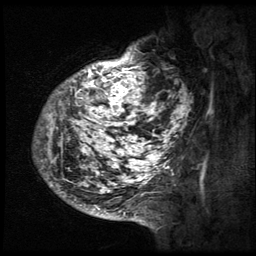
Breast MRI (dynamic contrast-enhanced), one sagittal slice. 3 images stored at this slice position (order not interpretable as contrast timing). 1.5 T. TE 4.2 ms, TR 9 ms. 2.5 mm slice thickness. 256 × 256 image matrix, field of view 180 × 180 mm. Patient: female, 50 years. From the clinical record (not read from this slice): setting: breast cancer imaged before/during neoadjuvant chemotherapy; receptor status: triple-negative.
Structures marked on this image (semi-automatically segmented with operator editing):
- analysis volume of interest (the breast-tissue region the enhancement analysis was run in; not a lesion): bounding box <32,39,194,212> (left, top, right, bottom; pixels)
- tumour enhancement mask (voxels above the 140 % enhancement threshold inside the analysis volume of interest): <33,46,191,212>